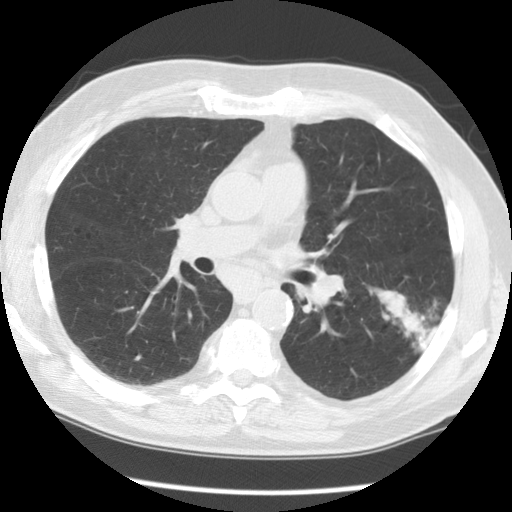
Chest CT (low-dose screening protocol), one axial image. First (baseline) screen. Lung window (W 1500 / L -600 HU). Standard (soft-tissue) reconstruction kernel (STANDARD). 120 kVp. Male participant, aged 71 years at enrolment. Former smoker at enrolment.
- Expert-annotated lung lesion, bounding box [x1, y1, x2, y2] px = [371, 280, 458, 365].
- The screening reader recorded 3 non-calcified nodules or masses ≥4 mm on this exam (left lower lobe, right upper lobe, right upper lobe); which of them this box marks is not recorded.
- Official screen result: positive, change unspecified: nodule(s) >= 4 mm or enlarging nodule(s), mass(es), or other non-specific abnormalities suspicious for lung cancer.